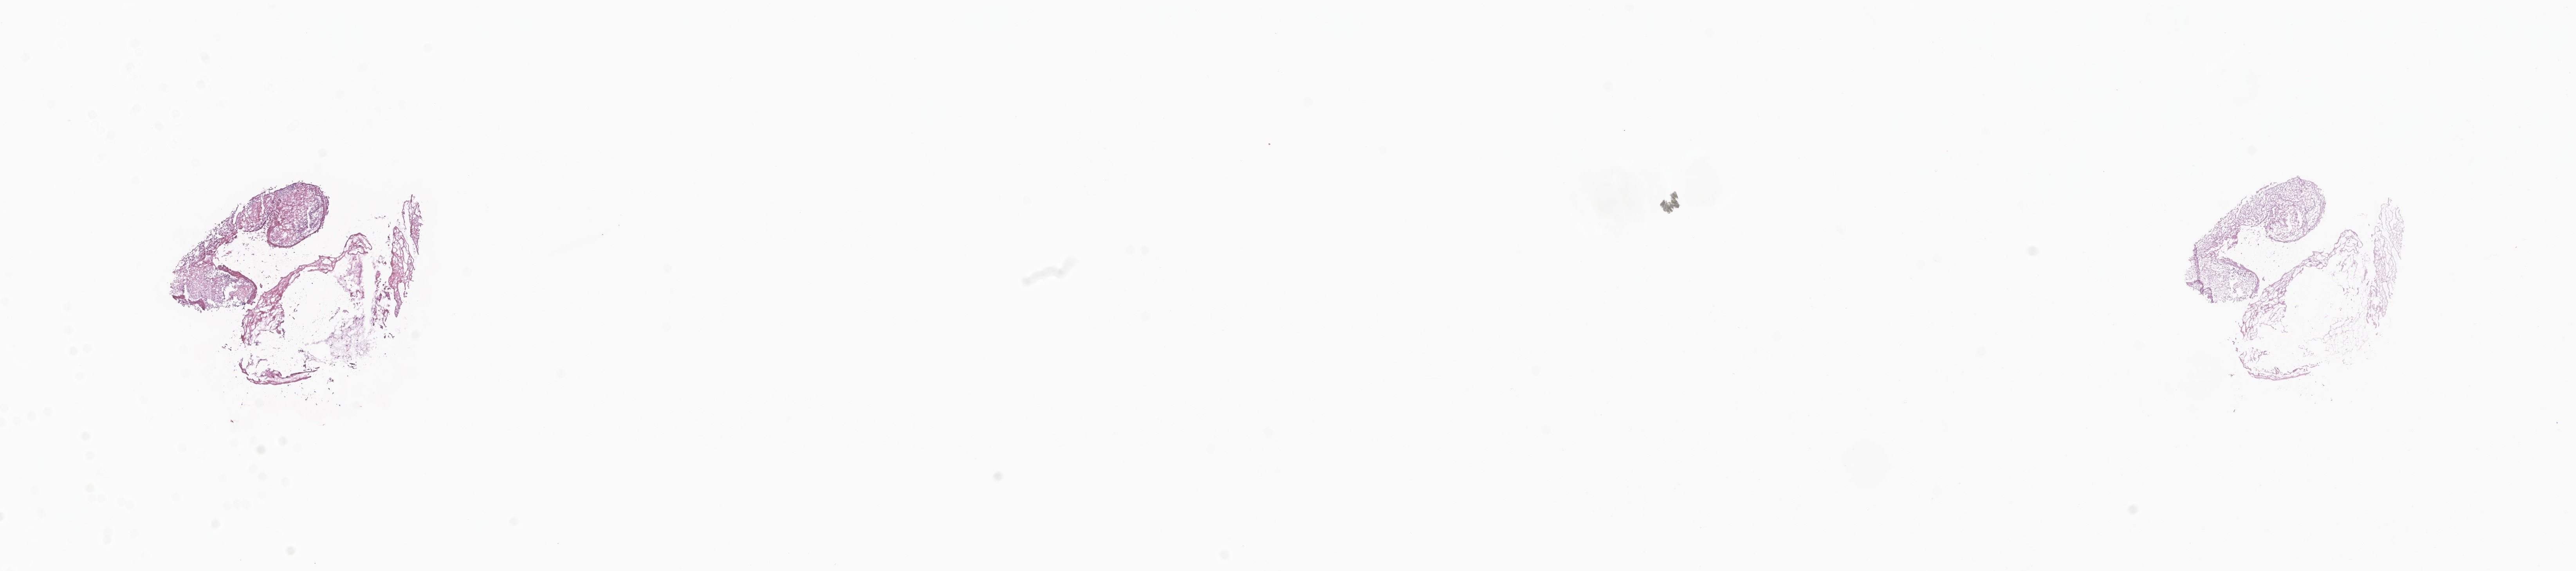
Hematoxylin and eosin (H&E) whole-slide image of tumor tissue from the posterior mediastinum — a low-resolution overview of the entire scanned area, about 27.7 x 6.2 mm; frozen section (OCT-embedded). Female patient, age 202 months (16 years 10 months).
Diagnosis: Malignant peripheral nerve sheath tumor, NOS.